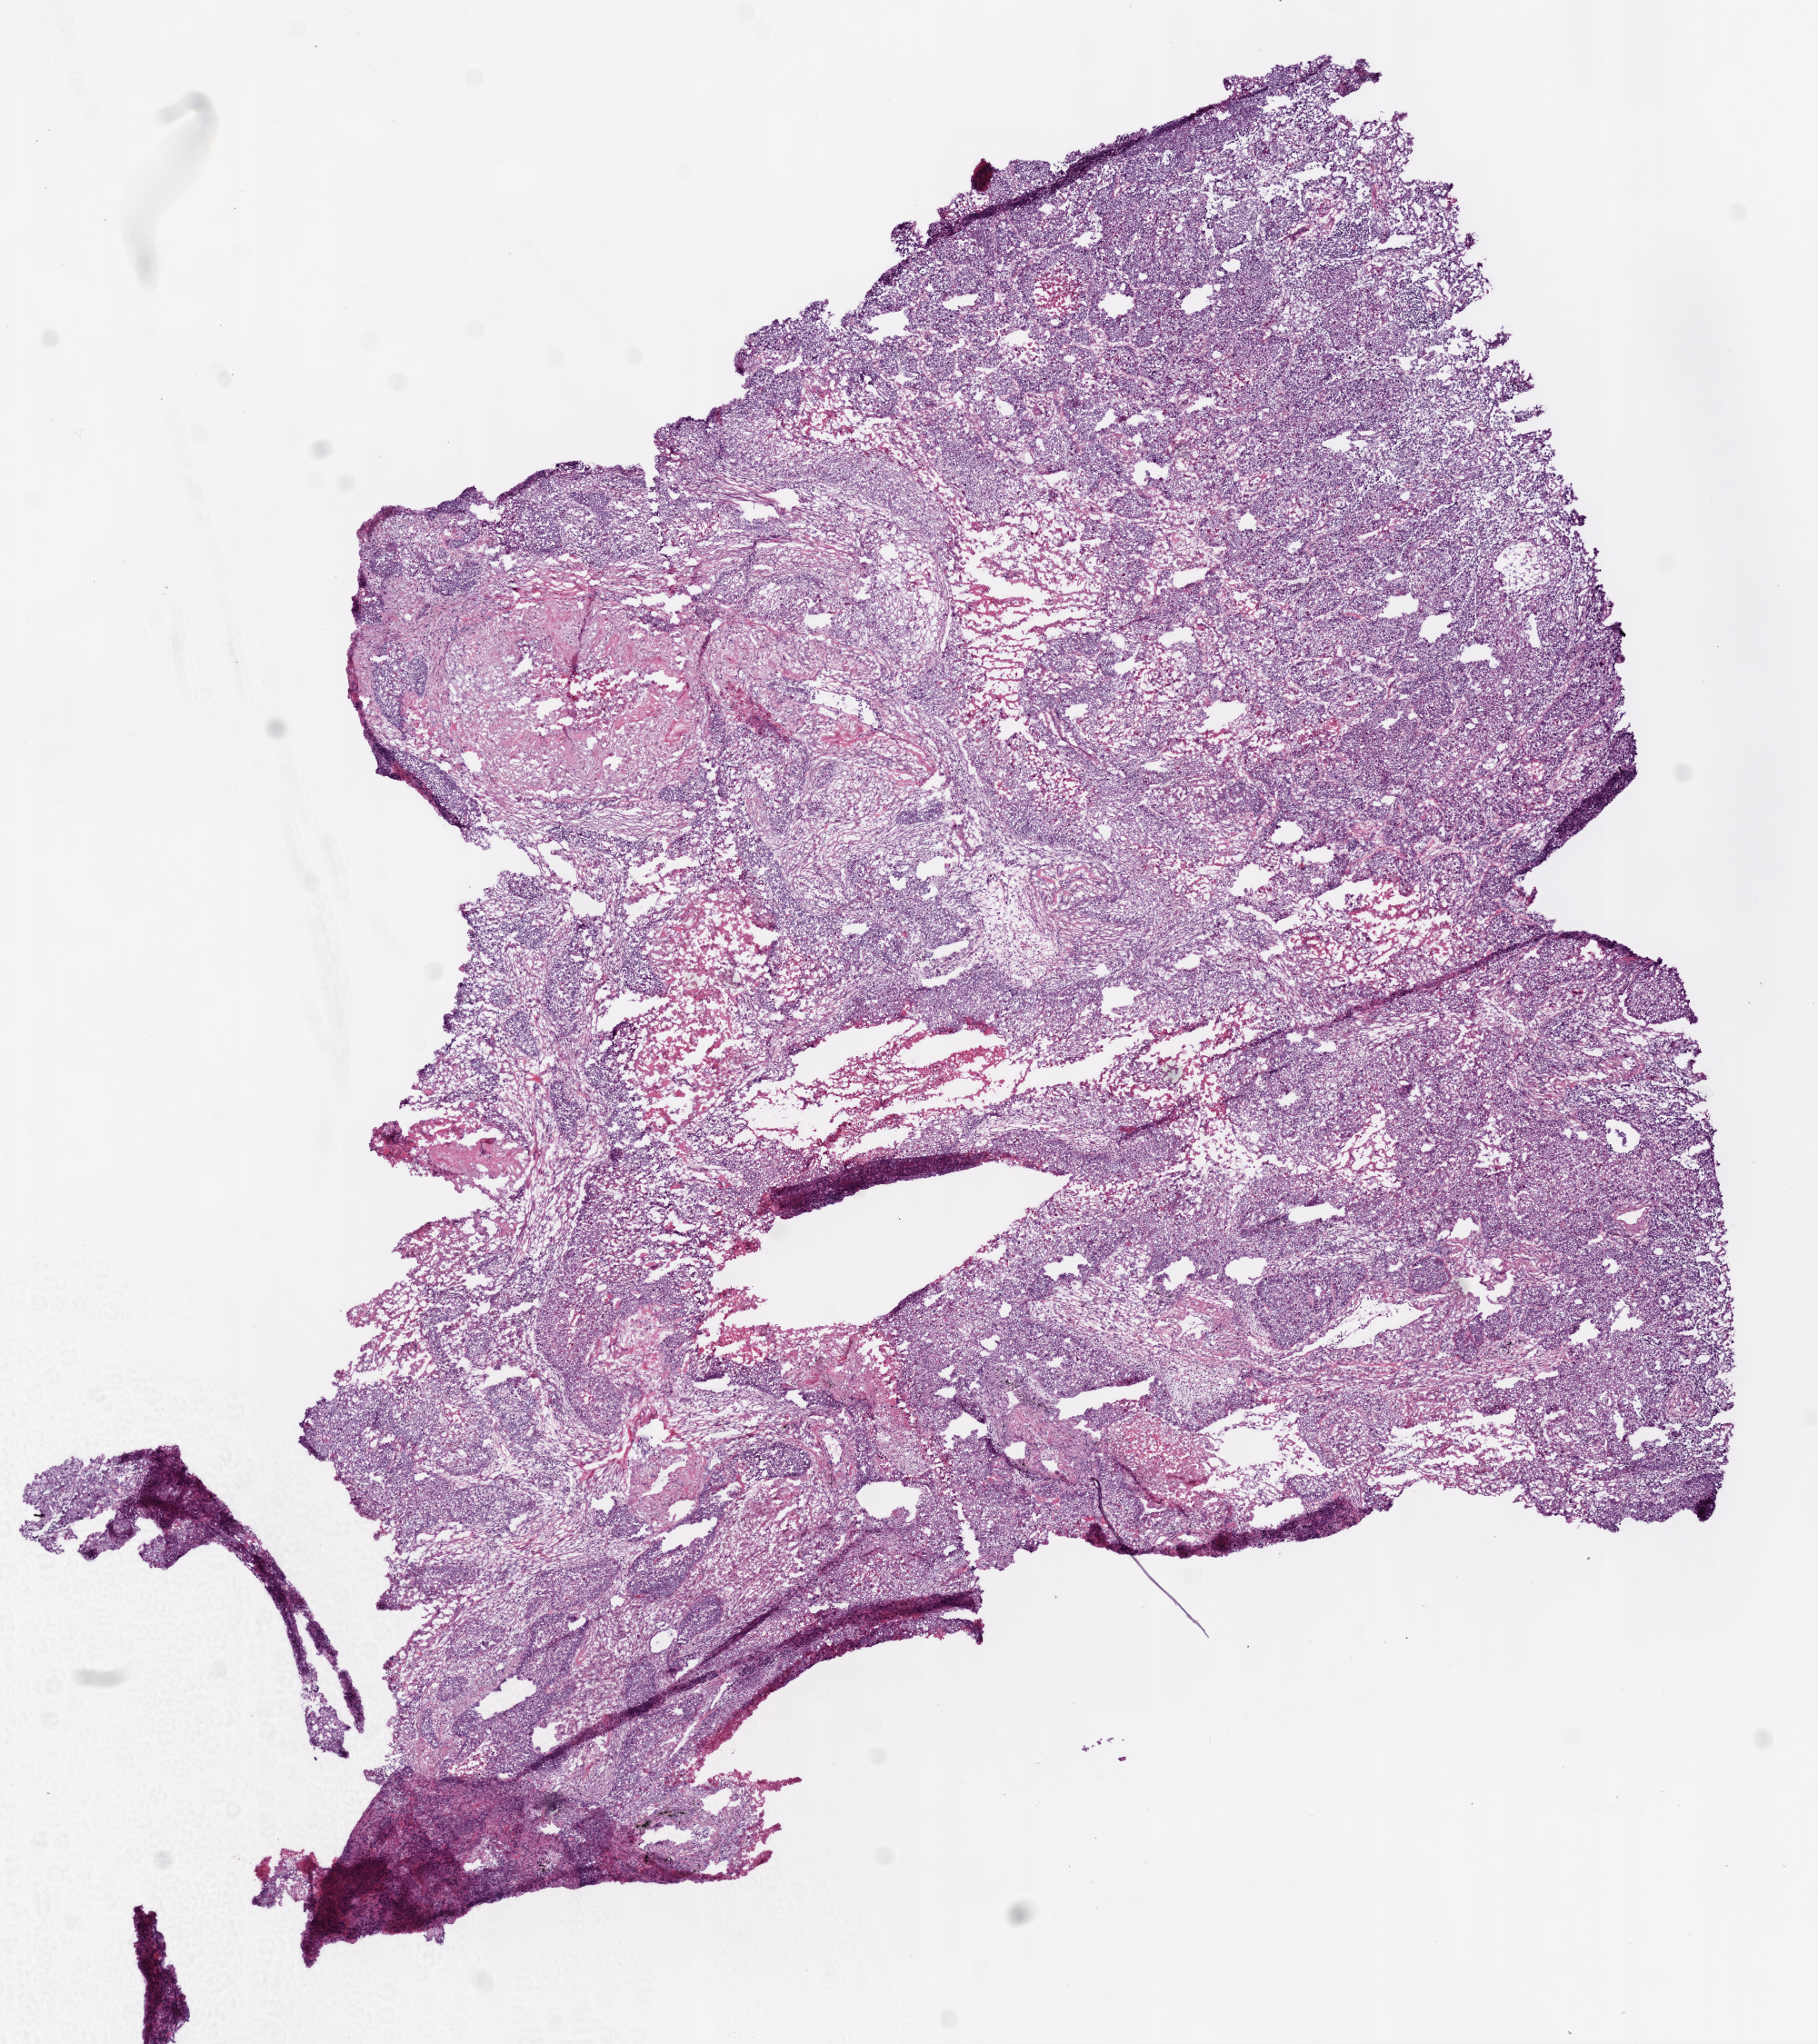
Digitized H&E tissue section (whole slide) — shown as a low-resolution overview of the whole scanned area (about 8.0 x 9.0 mm). Frozen section. Sample: primary tumour, lung. Male patient; age at initial diagnosis 73 years. Composition of this section per pathologist review: tumour cells 69%, tumour nuclei 75%.
Histologic diagnosis: Squamous cell carcinoma, NOS (lower lobe, lung).